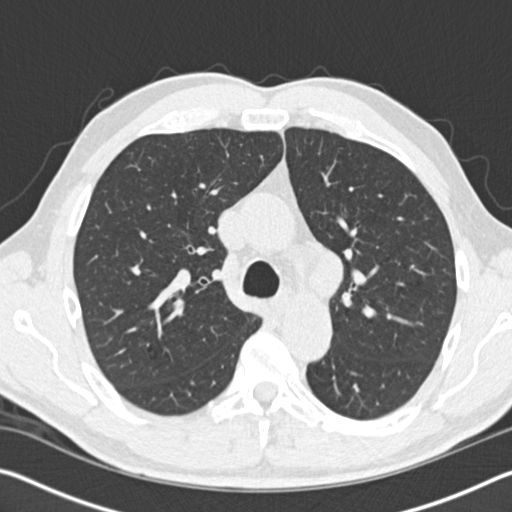
Low-dose screening chest CT, axial slice; baseline annual screen; lung window (W 1500 / L -600 HU); 2 mm slice thickness; 120 kVp; slice 59 of 162 in the series; 512 × 512 image matrix, field of view 340 × 340 mm. Male participant, aged 61 years at enrolment. Former smoker at enrolment.
• Expert-annotated lung lesion, bounding box (x1, y1, x2, y2) in pixels: (345, 276, 372, 312).
• The screening reader recorded 2 non-calcified nodules or masses ≥4 mm on this exam (right middle lobe, left upper lobe); which of them this box marks is not recorded.
• Later outcome: lung cancer diagnosed 183 days after this screen — small cell carcinoma, NOS, left upper lobe, stage IIIB (AJCC 6th edition), 100 mm at pathology.